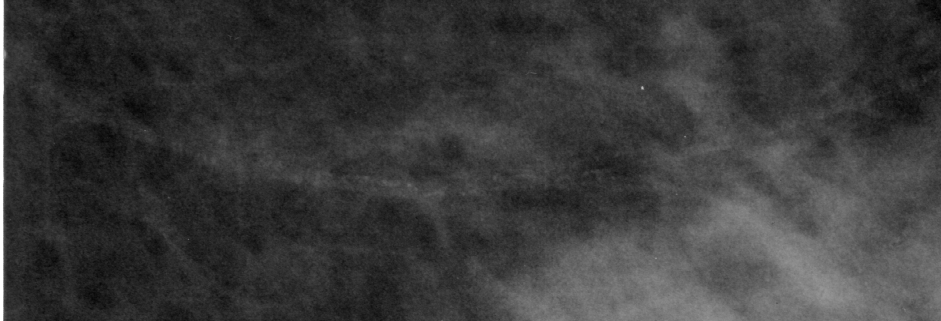
Region of interest cut from a scanned film mammogram (one marked finding); left breast; MLO view; BI-RADS breast density category 3 (scale 1–4).
Calcifications, morphology vascular; BI-RADS assessment category 2; benign; no additional work-up was recommended (benign without callback).